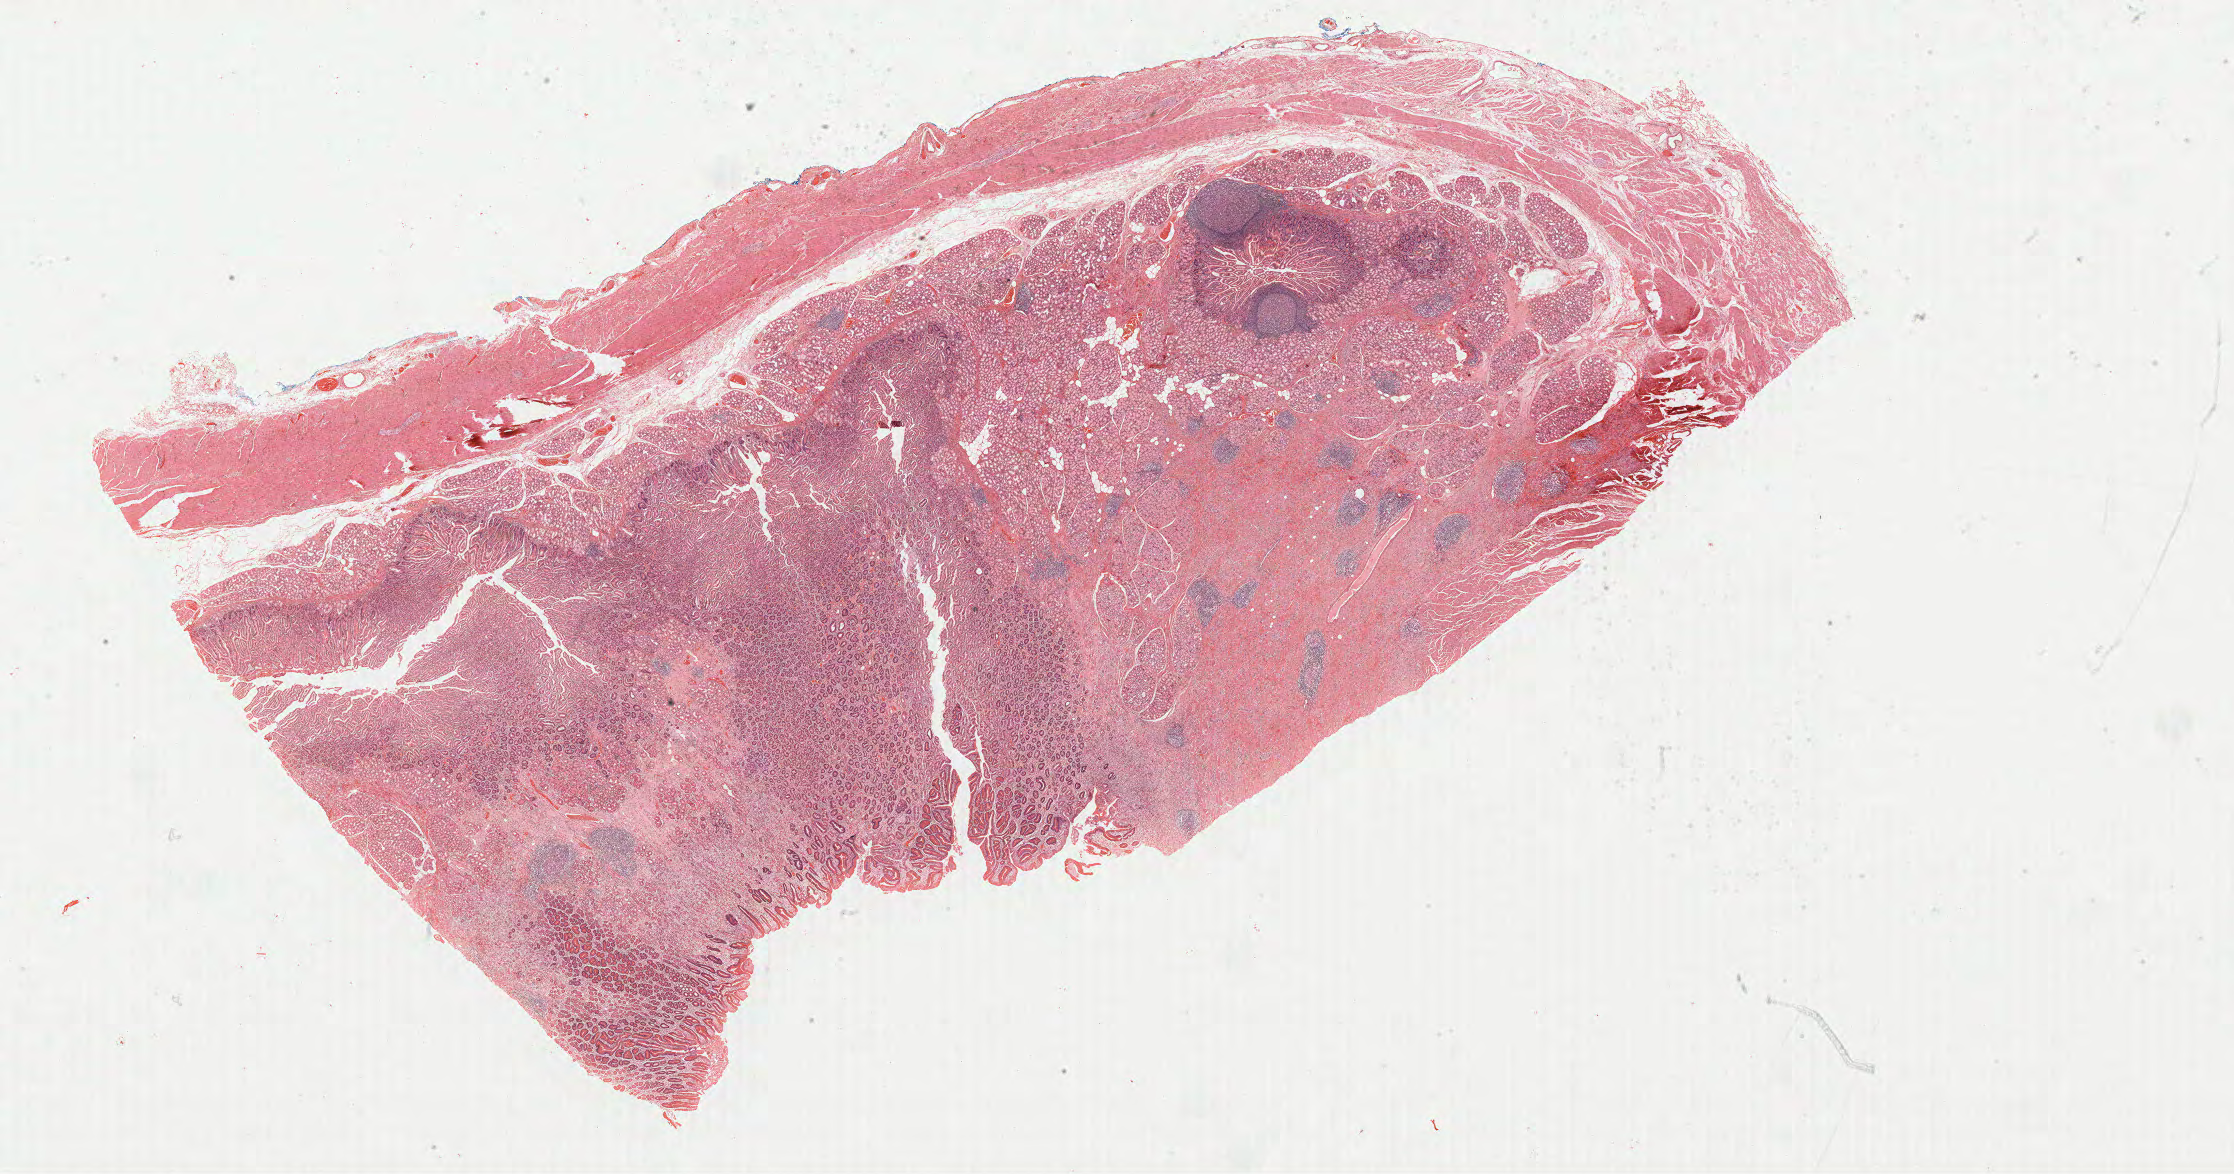
Hematoxylin and eosin (H&E) stained whole-slide image — a low-resolution overview of the entire scanned area, about 35.9 x 18.9 mm, formalin-fixed paraffin-embedded (FFPE) diagnostic section, sample: primary tumour, stomach. Female, age 59 years at initial diagnosis. Histologic grade: G3 (poorly differentiated).
• histologic diagnosis: Carcinoma, diffuse type (gastric antrum)
• AJCC pathologic stage: IB (6th edition)